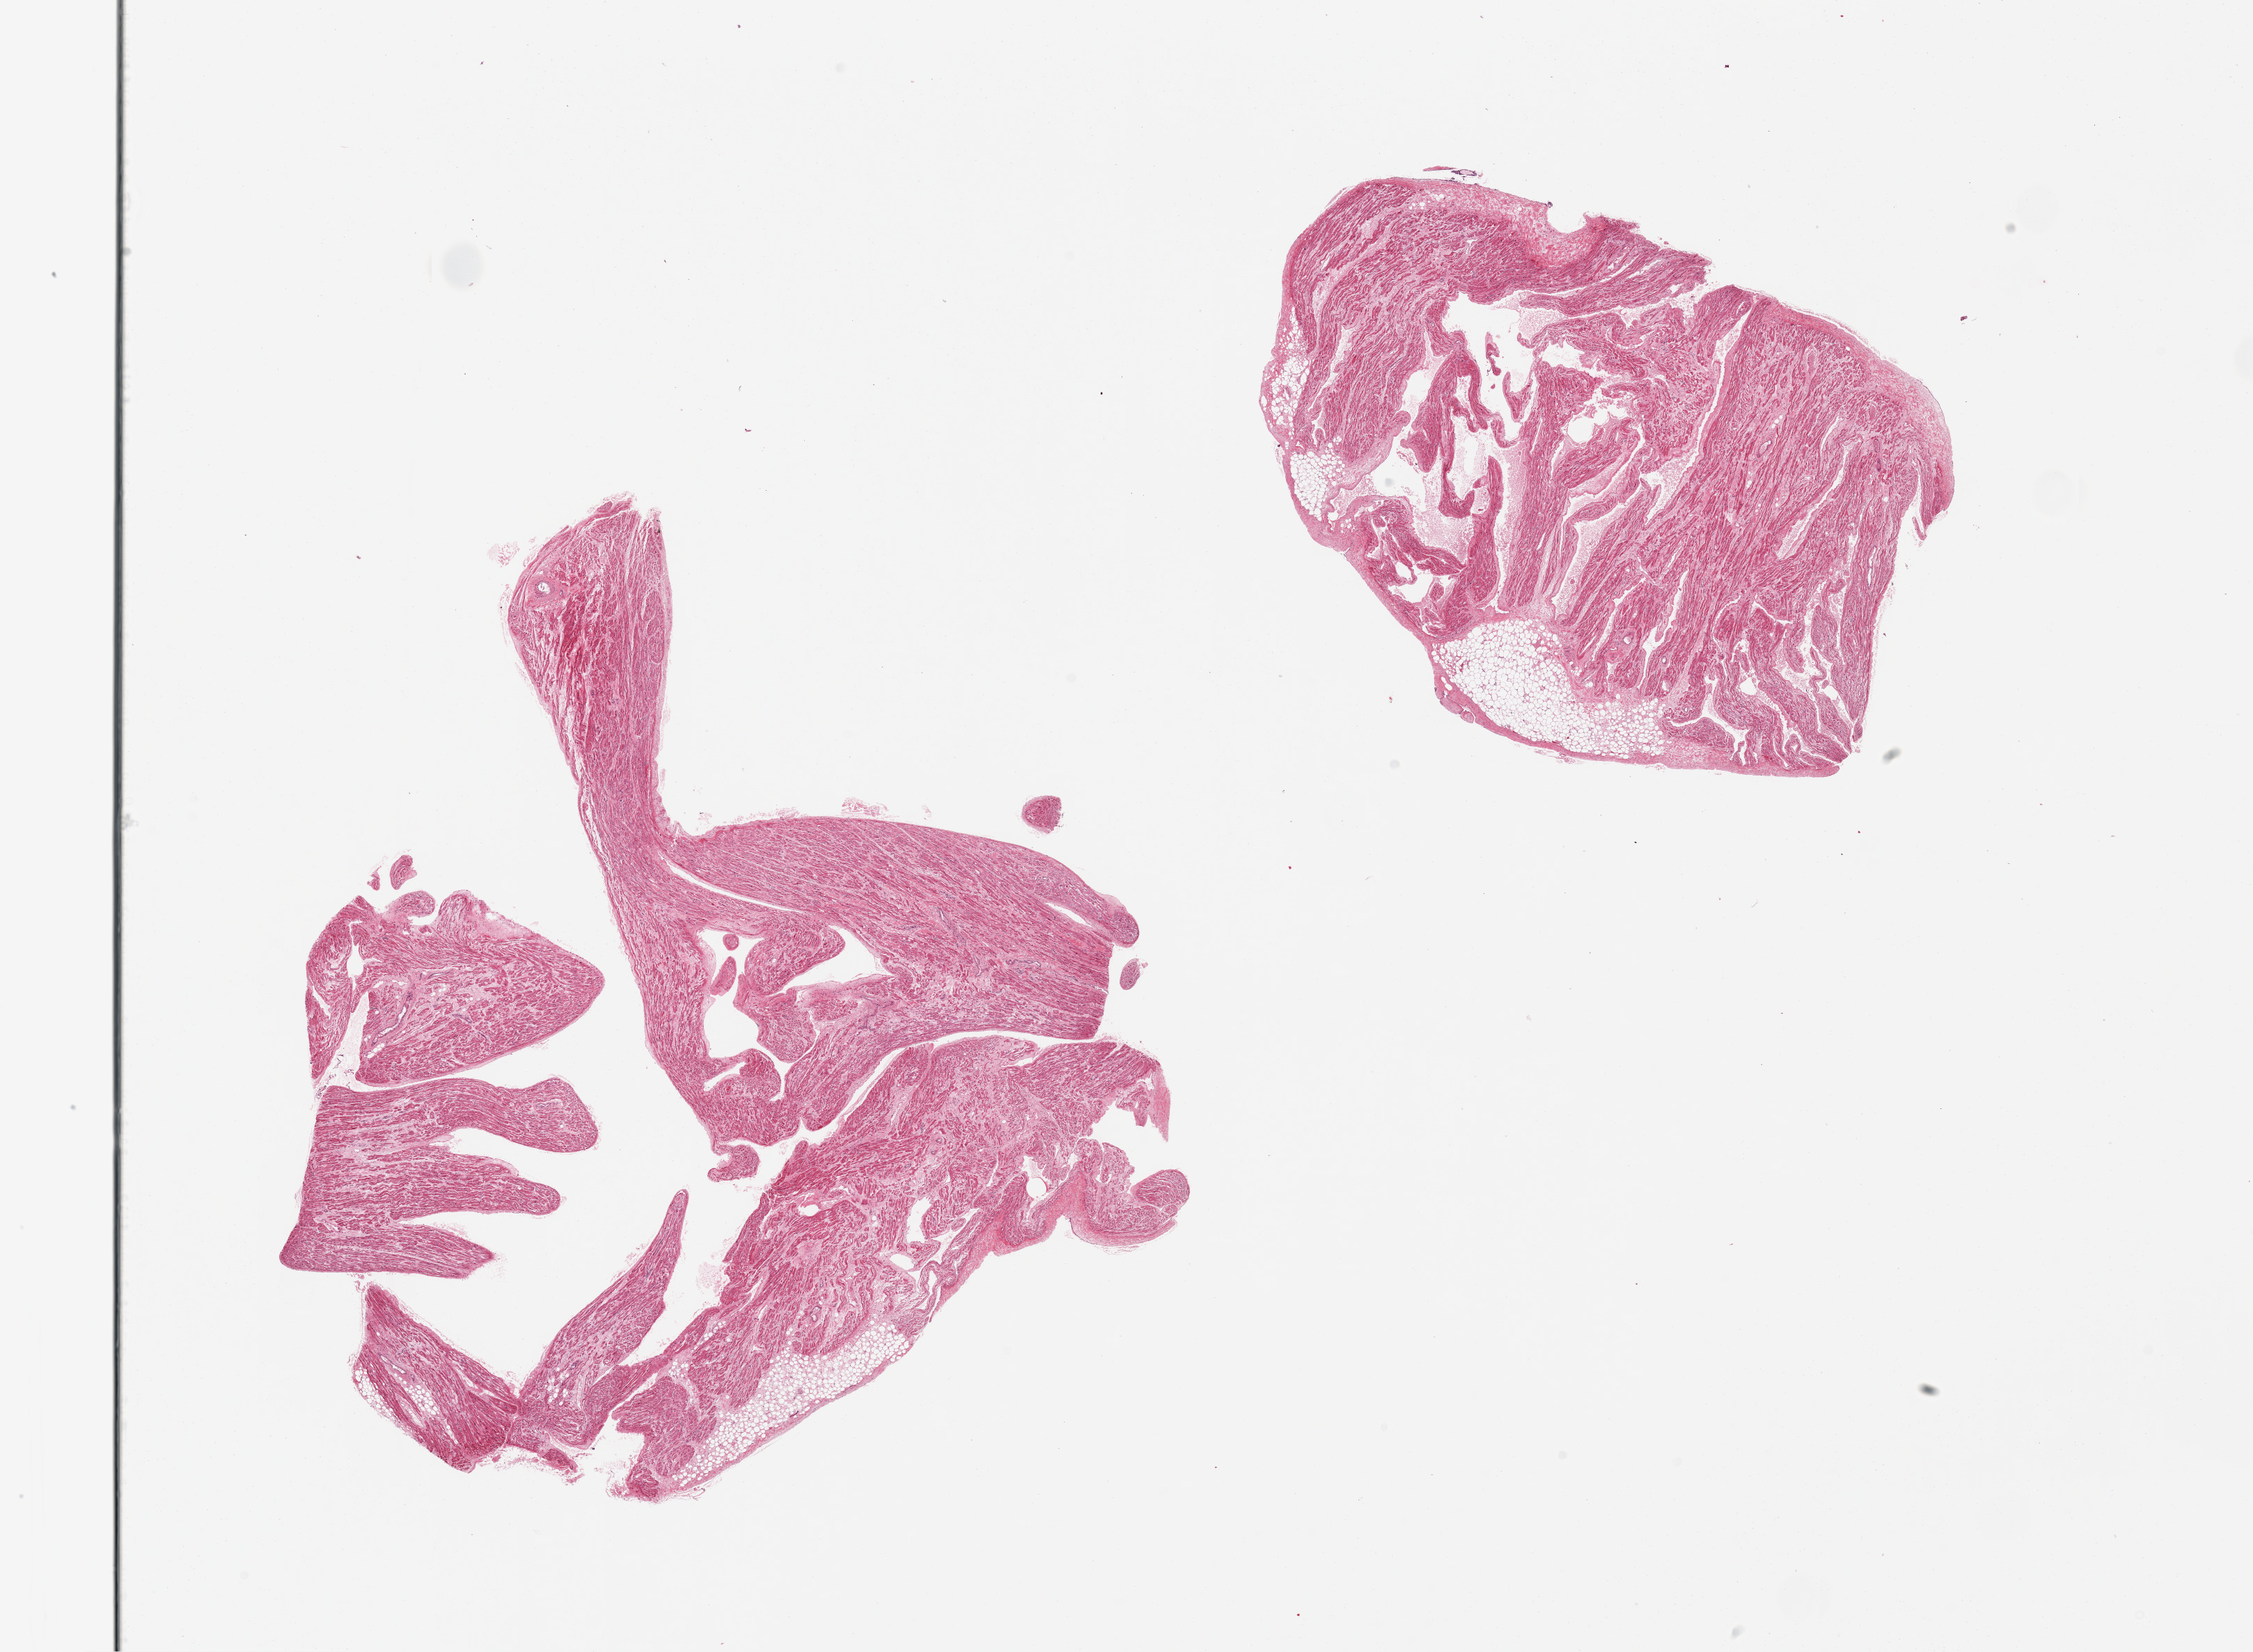
Whole-slide image, hematoxylin and eosin (H&E) stain, brightfield — shown as a low-resolution overview of the whole scanned area (about 25.6 x 18.8 mm, from a 20x scan). PAXgene-fixed paraffin-embedded (PFPE) section. Sampled site (target tissue): auricular appendage. Tissue donor sample. Male donor.
Review note (as recorded): 2 pieces.